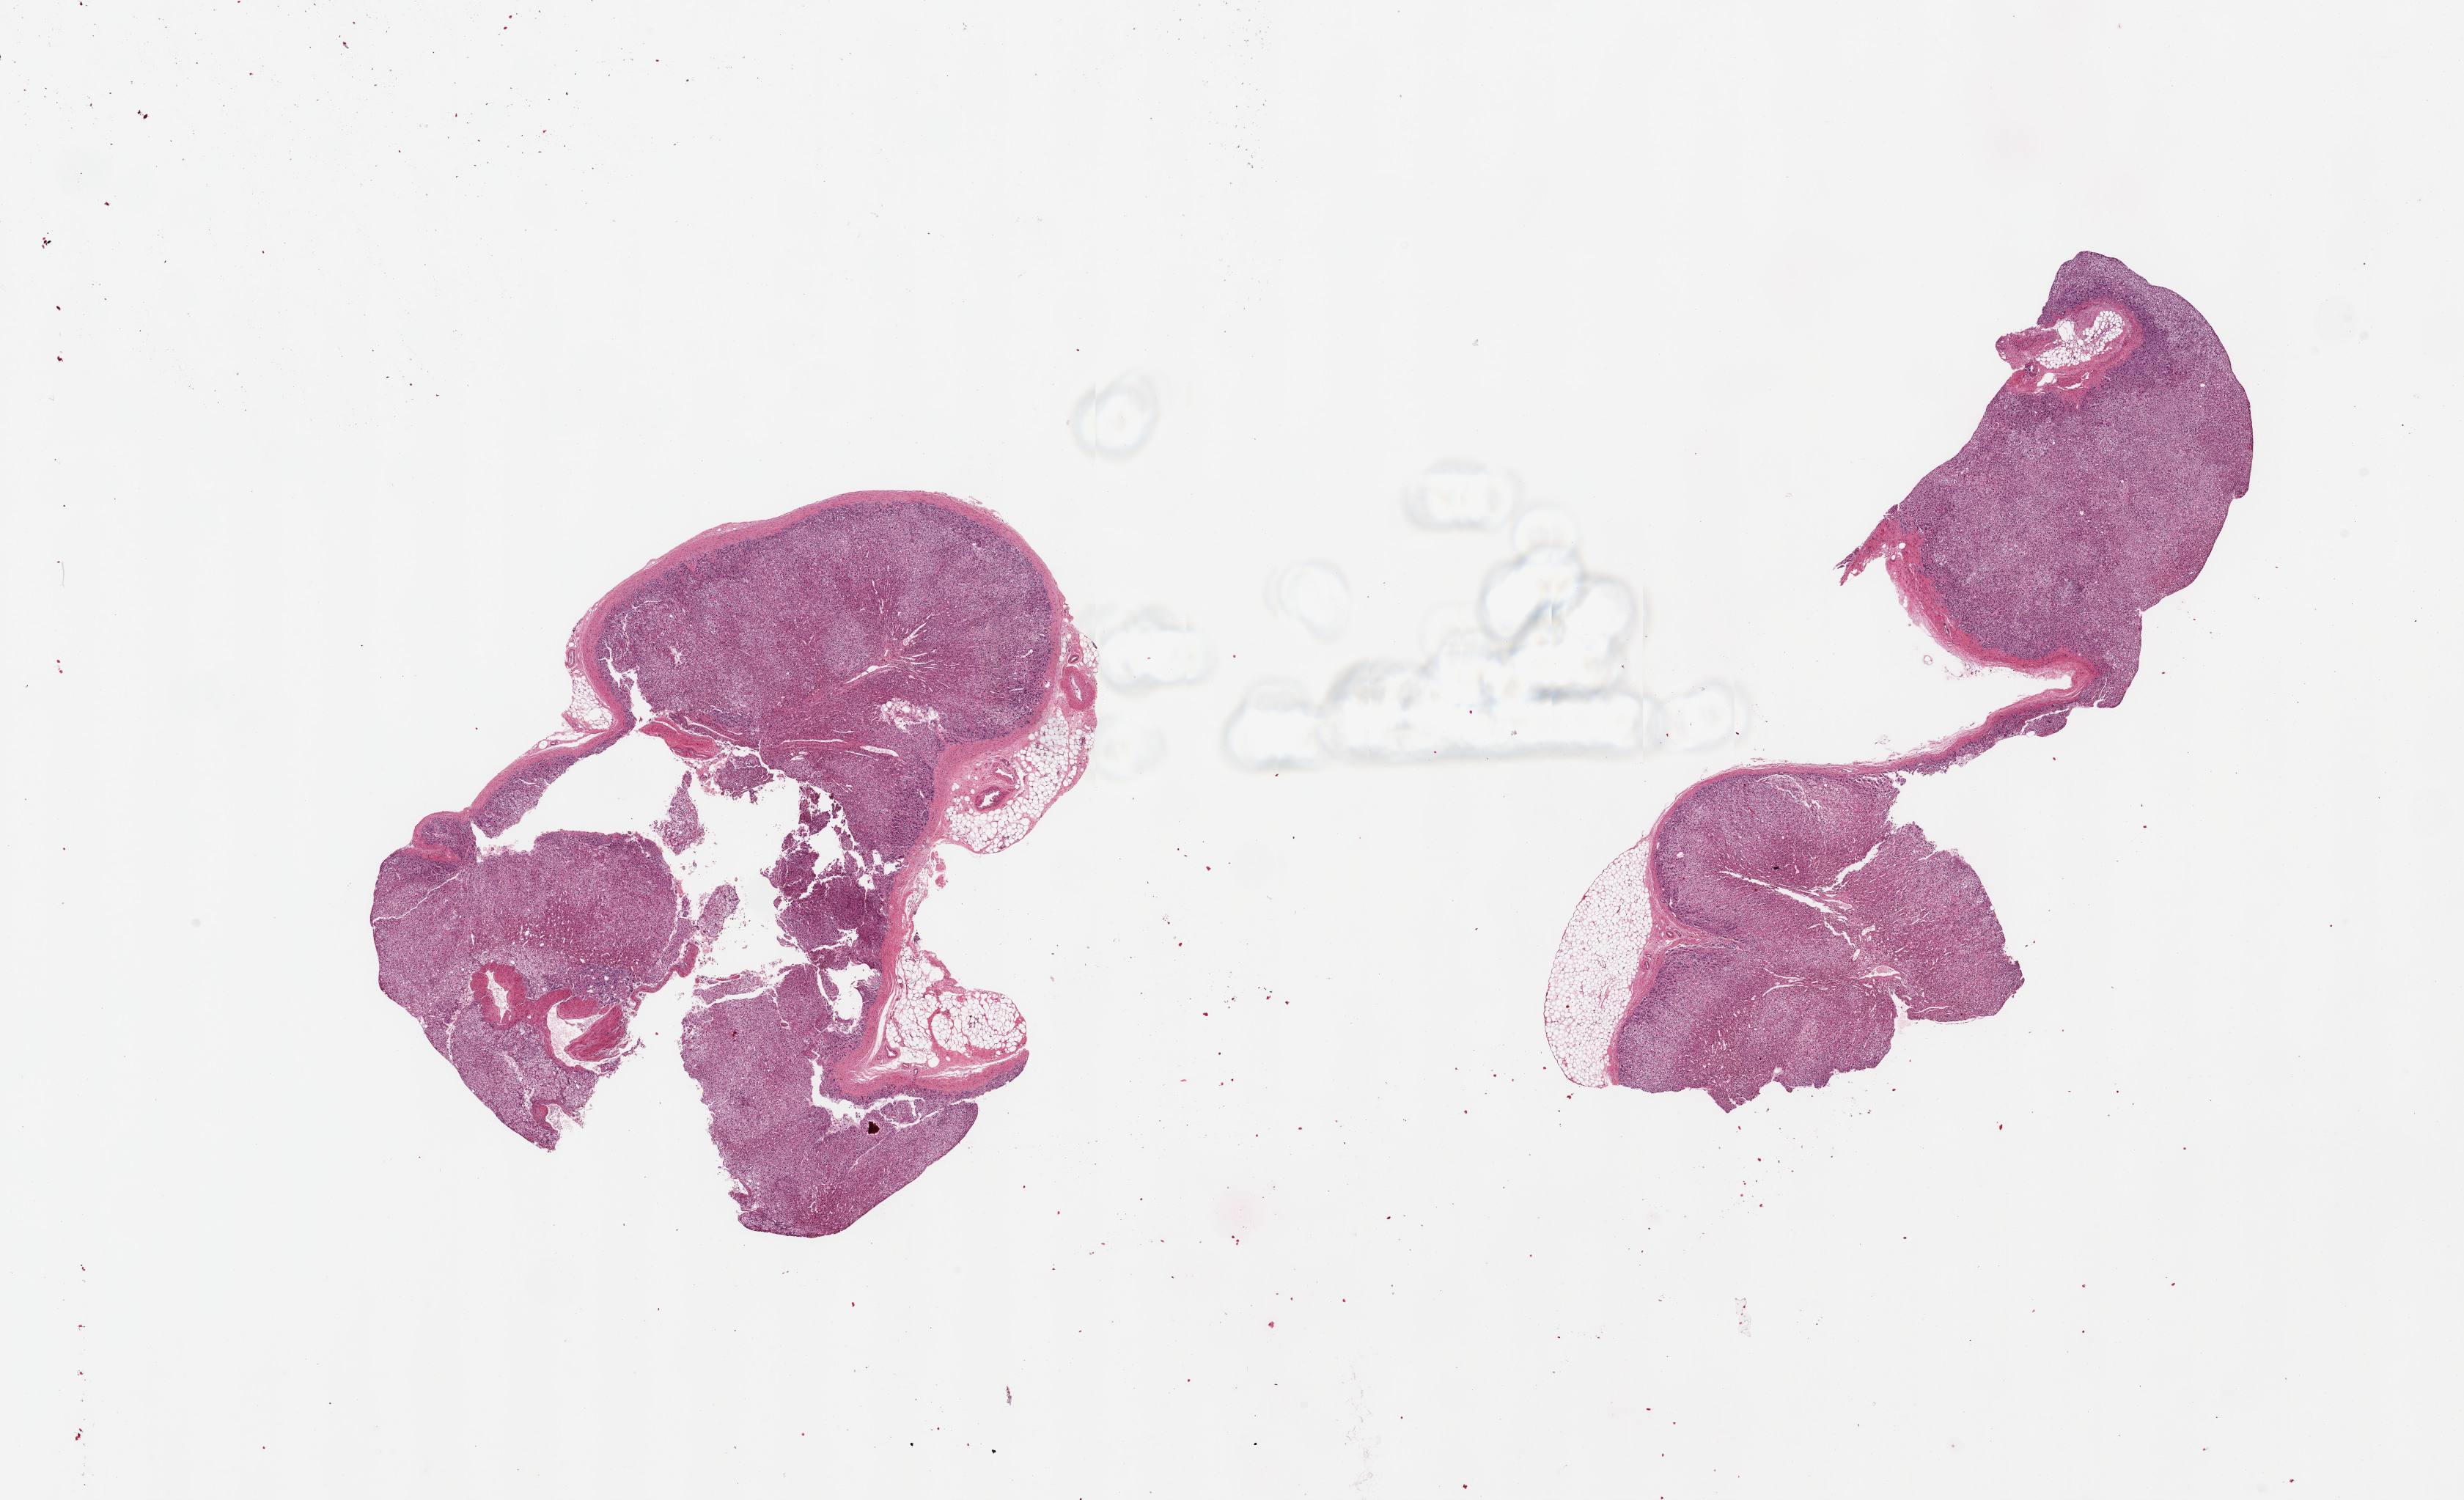
Whole-slide image, hematoxylin and eosin (H&E) stain — low-resolution overview of the scanned area, about 26.6 x 16.2 mm. PAXgene-fixed, paraffin-embedded tissue. Sampled site (target tissue): adrenal gland. Tissue donor sample.
• review note (as recorded): 2 pieces; both include small attachment of fat, predominantly cortex with small portion of medulla in 1 piece